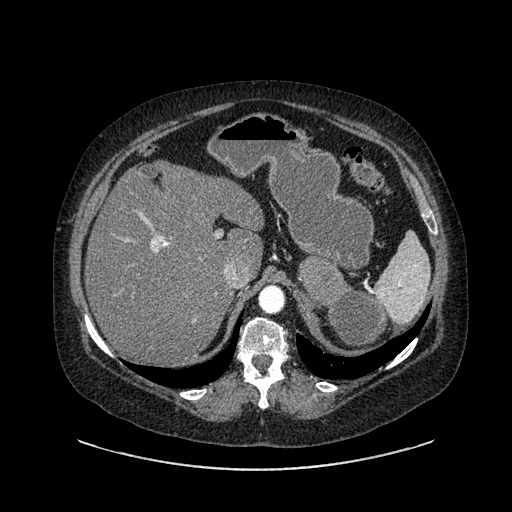
Contrast-enhanced abdominal CT, one axial slice; slice 620 of 769 in the series (ordered by position); reconstruction kernel SOFT; 120 kVp; intravenous contrast given; soft-tissue window (W 400 / L 40 HU); 0.62 mm slice thickness; 512 × 512 image matrix. Female patient, age 61 years. From the clinical record (not read from this slice): diagnosis: adrenocortical carcinoma; tumour side: left adrenal; tumour size at pathology: 13 cm; Ki-67 index: 79 %; stage (as recorded): 2.
Structures marked on this image (semi-automatic segmentation, software-assisted and operator-edited):
- mass: bounding box <299,259,389,348> (left, top, right, bottom; pixels)